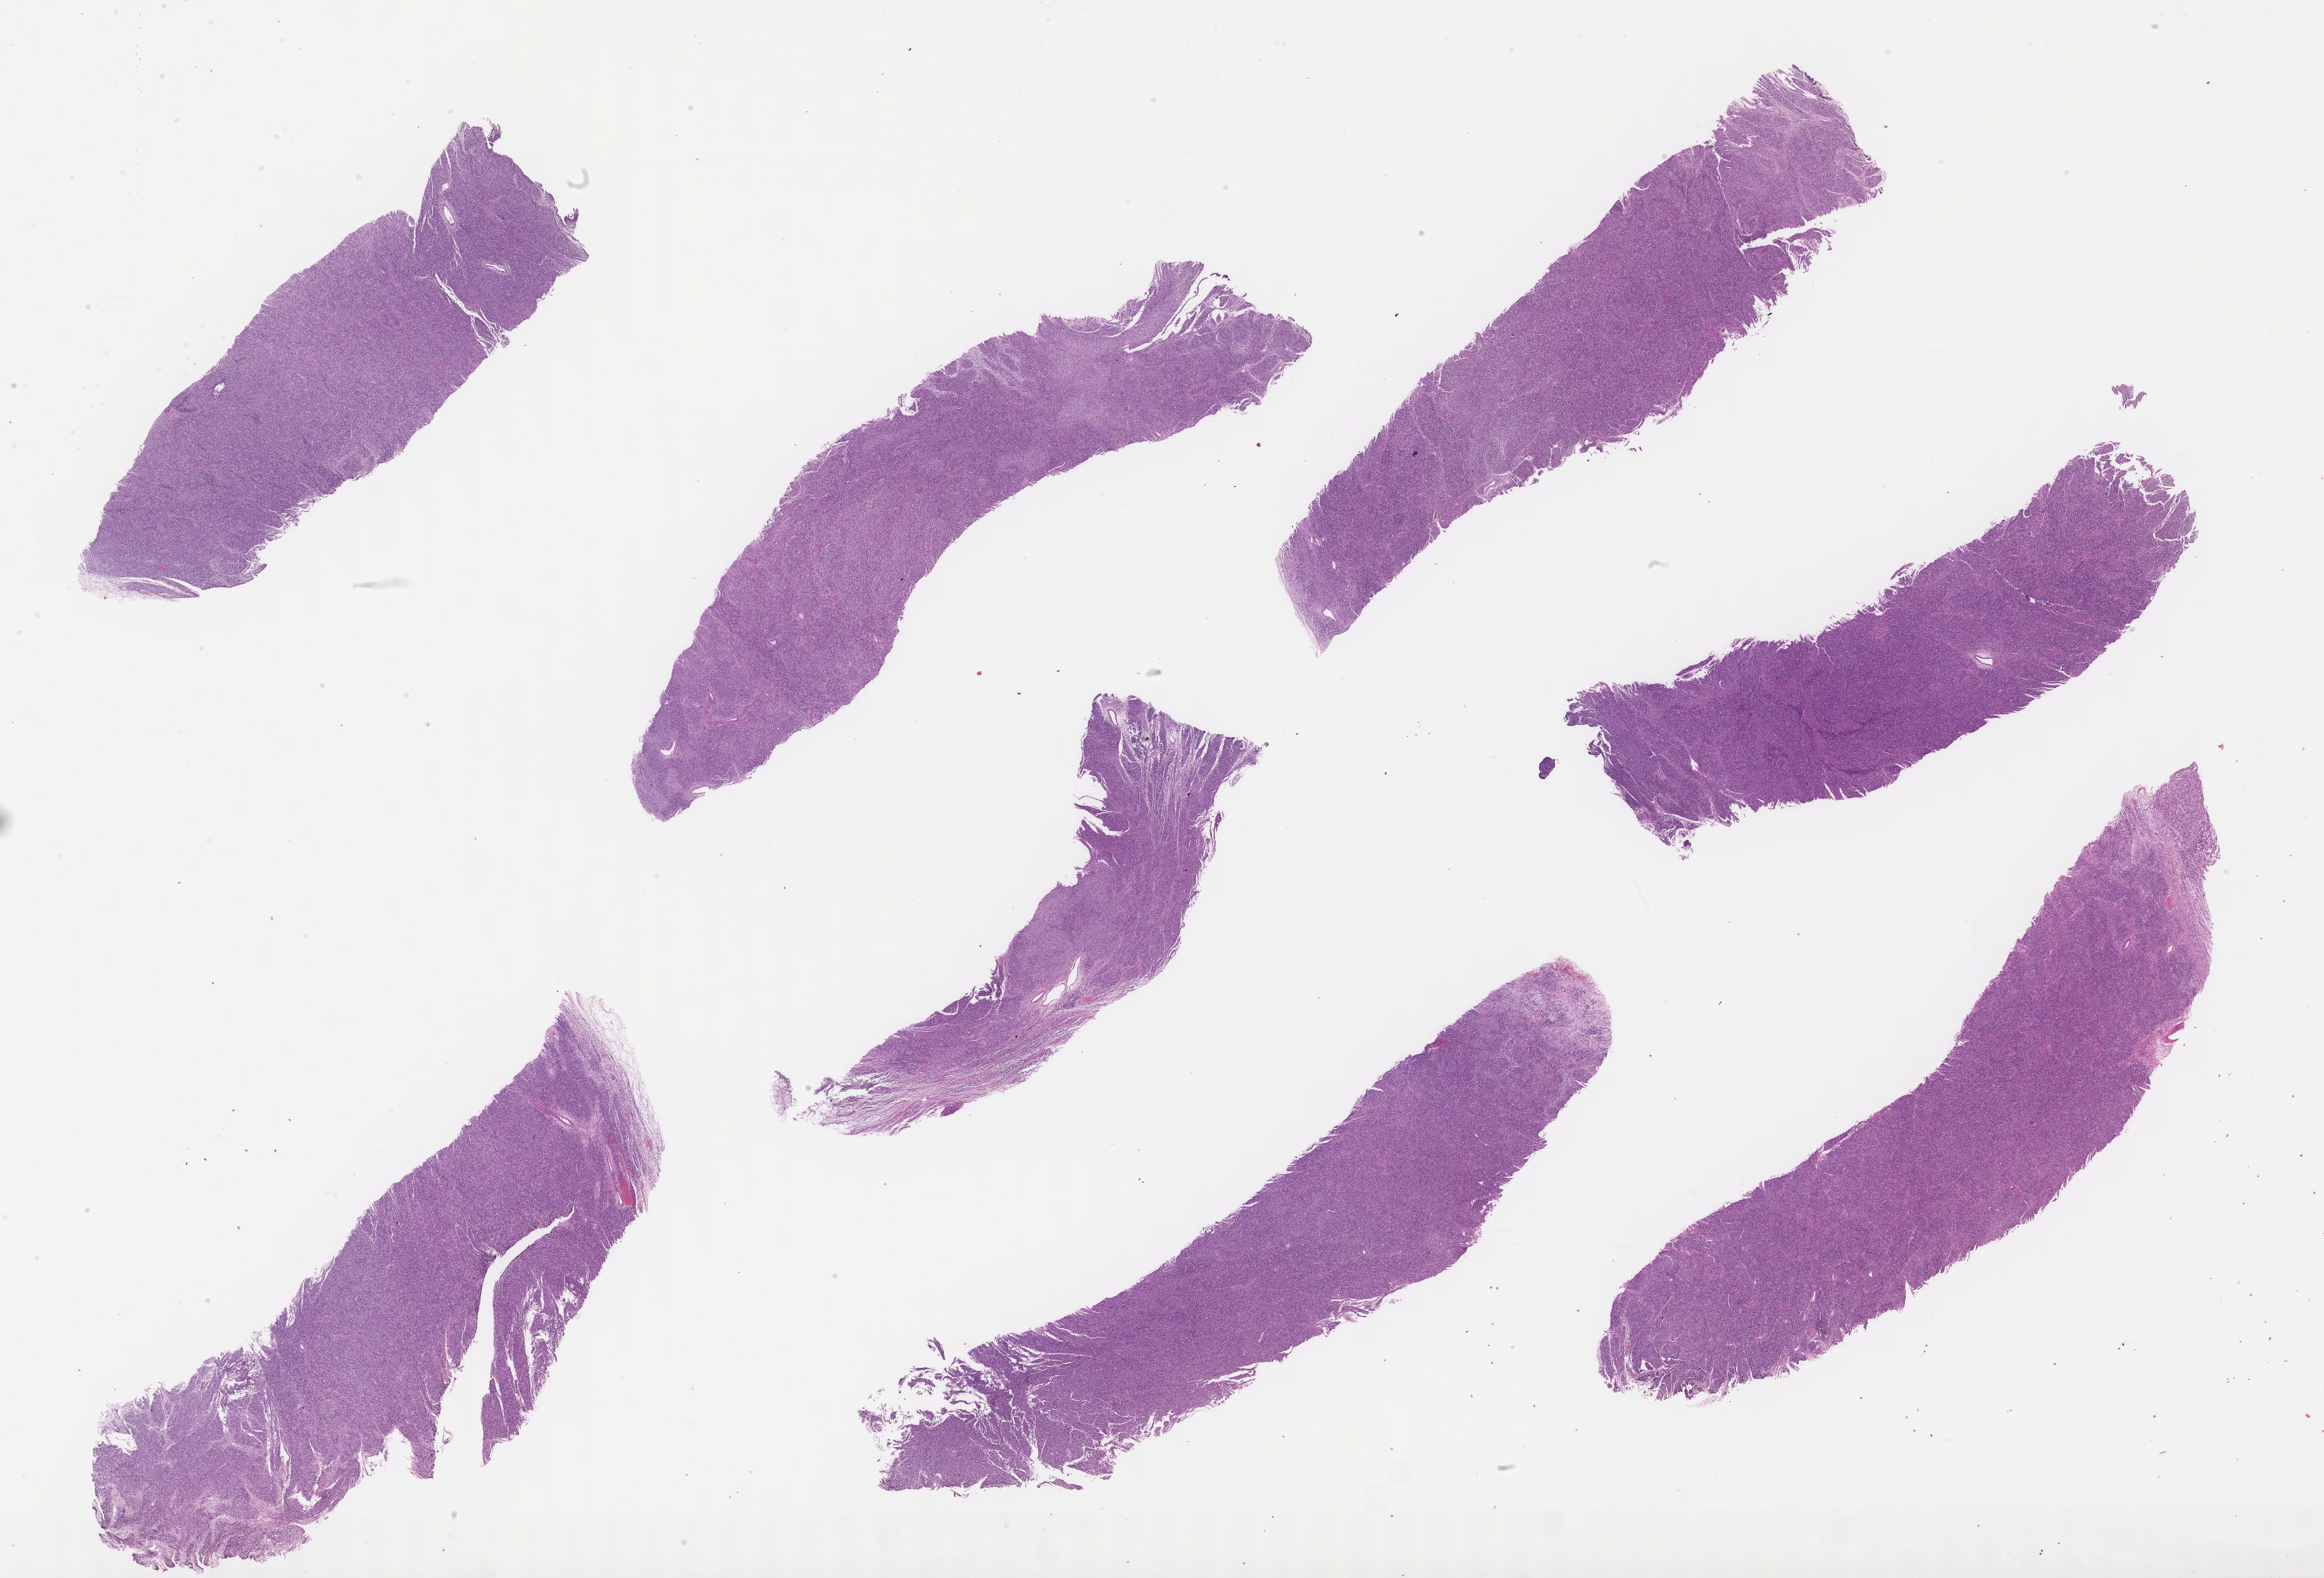
Whole-slide image, haematoxylin and eosin stain of tumor tissue — low-resolution overview of the scanned area, about 29.7 x 20.2 mm. Formalin-fixed paraffin-embedded section. Sample anatomic site: paratesticular, left. Male patient, age at diagnosis 2.1 years.
Metastatic status at presentation (as recorded): non-metastatic (confirmed). Stage (as recorded): 1. Primary site (case record): testis-paratesticular. Diagnosis: rhabdomyosarcoma; histological classification: embryonal rhabdomyosarcoma.